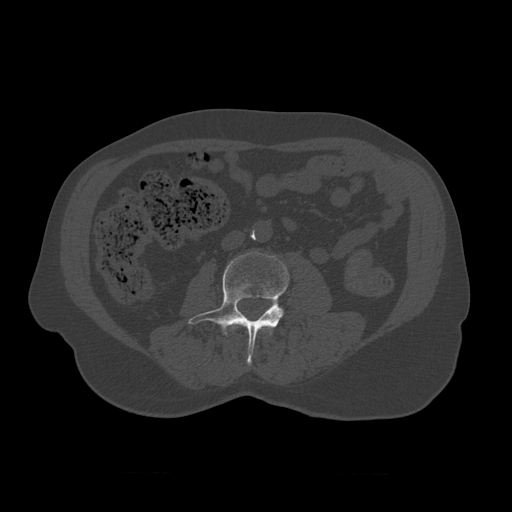
CT including the spine, one axial slice. Slice 303 of 450 in the series (ordered by position). Reconstruction kernel STANDARD. 120 kVp. Bone window (W 1800 / L 400 HU). 1.25 mm slice thickness. 512 × 512 image matrix, field of view 405 × 405 mm. Patient age 75 years. From the clinical record (not read from this slice): primary cancer: prostate.
Structures marked on this image (semi-automatic segmentation, software-assisted and operator-edited):
- L2 vertebra: box from (x=233, y=323) to (x=264, y=333) px
- L3 vertebra: (x=188, y=252)–(x=290, y=366)